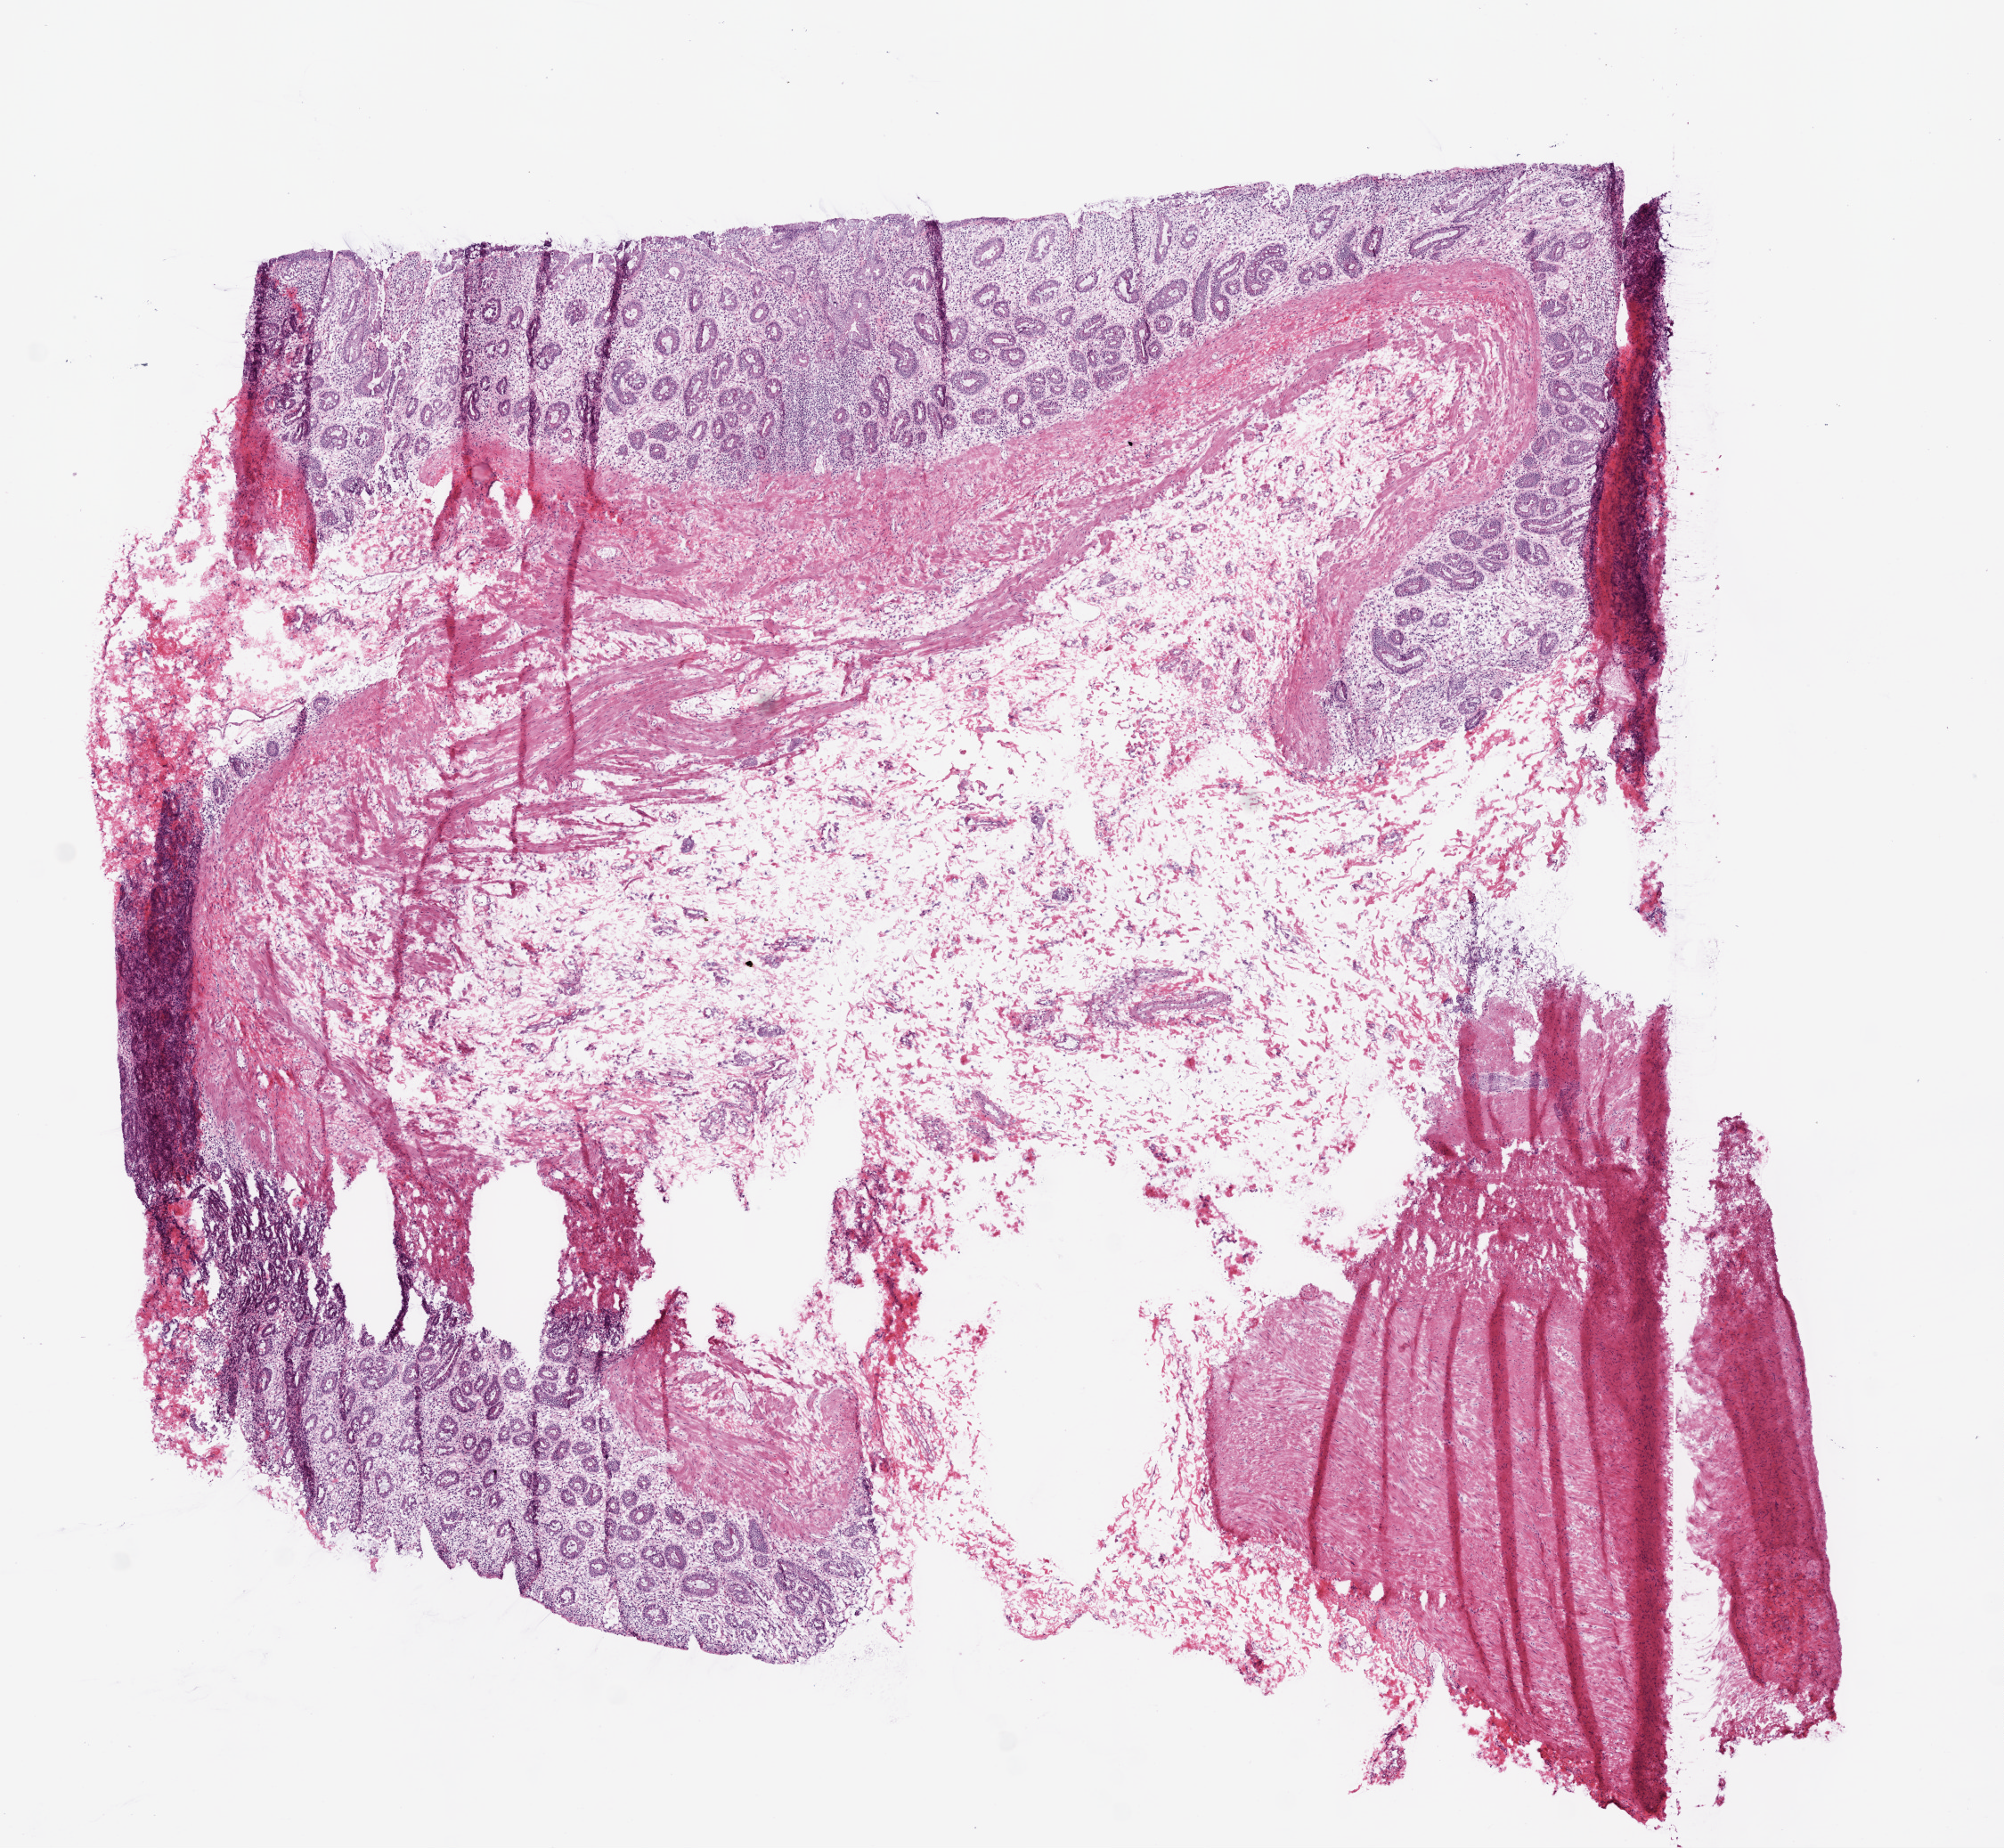
Whole-slide histology image, H&E-stained — a low-resolution overview of the entire scanned area, about 9.0 x 8.3 mm (acquisition: 20x scan). Frozen section. Sample: solid tissue normal (non-tumour tissue), rectum. Male patient; age at initial diagnosis 39 years.
This section: solid tissue normal sample (biorepository sample class). Patient diagnosis: Adenocarcinoma, NOS (rectosigmoid junction).